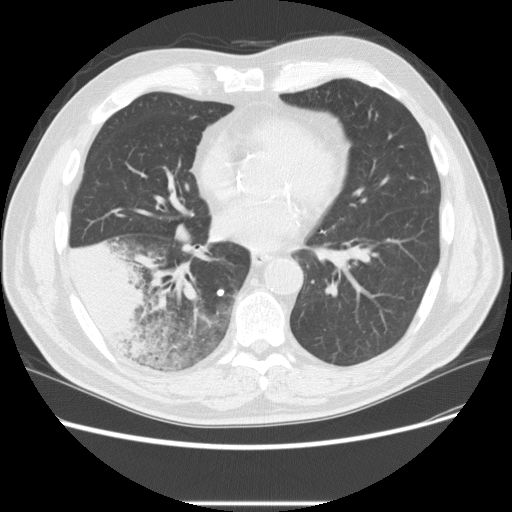
Low-dose screening chest CT, one axial slice; position 100 of 233 along the scan axis; reconstruction kernel STANDARD; lung window (W 1500 / L -600 HU); 512 × 512 image matrix, field of view 380 × 380 mm.
Outlined on this slice (manually delineated by an expert):
- lesion 3 (tumor, lower lobe of right lung): bounding box <66,240,147,345> (left, top, right, bottom; pixels)